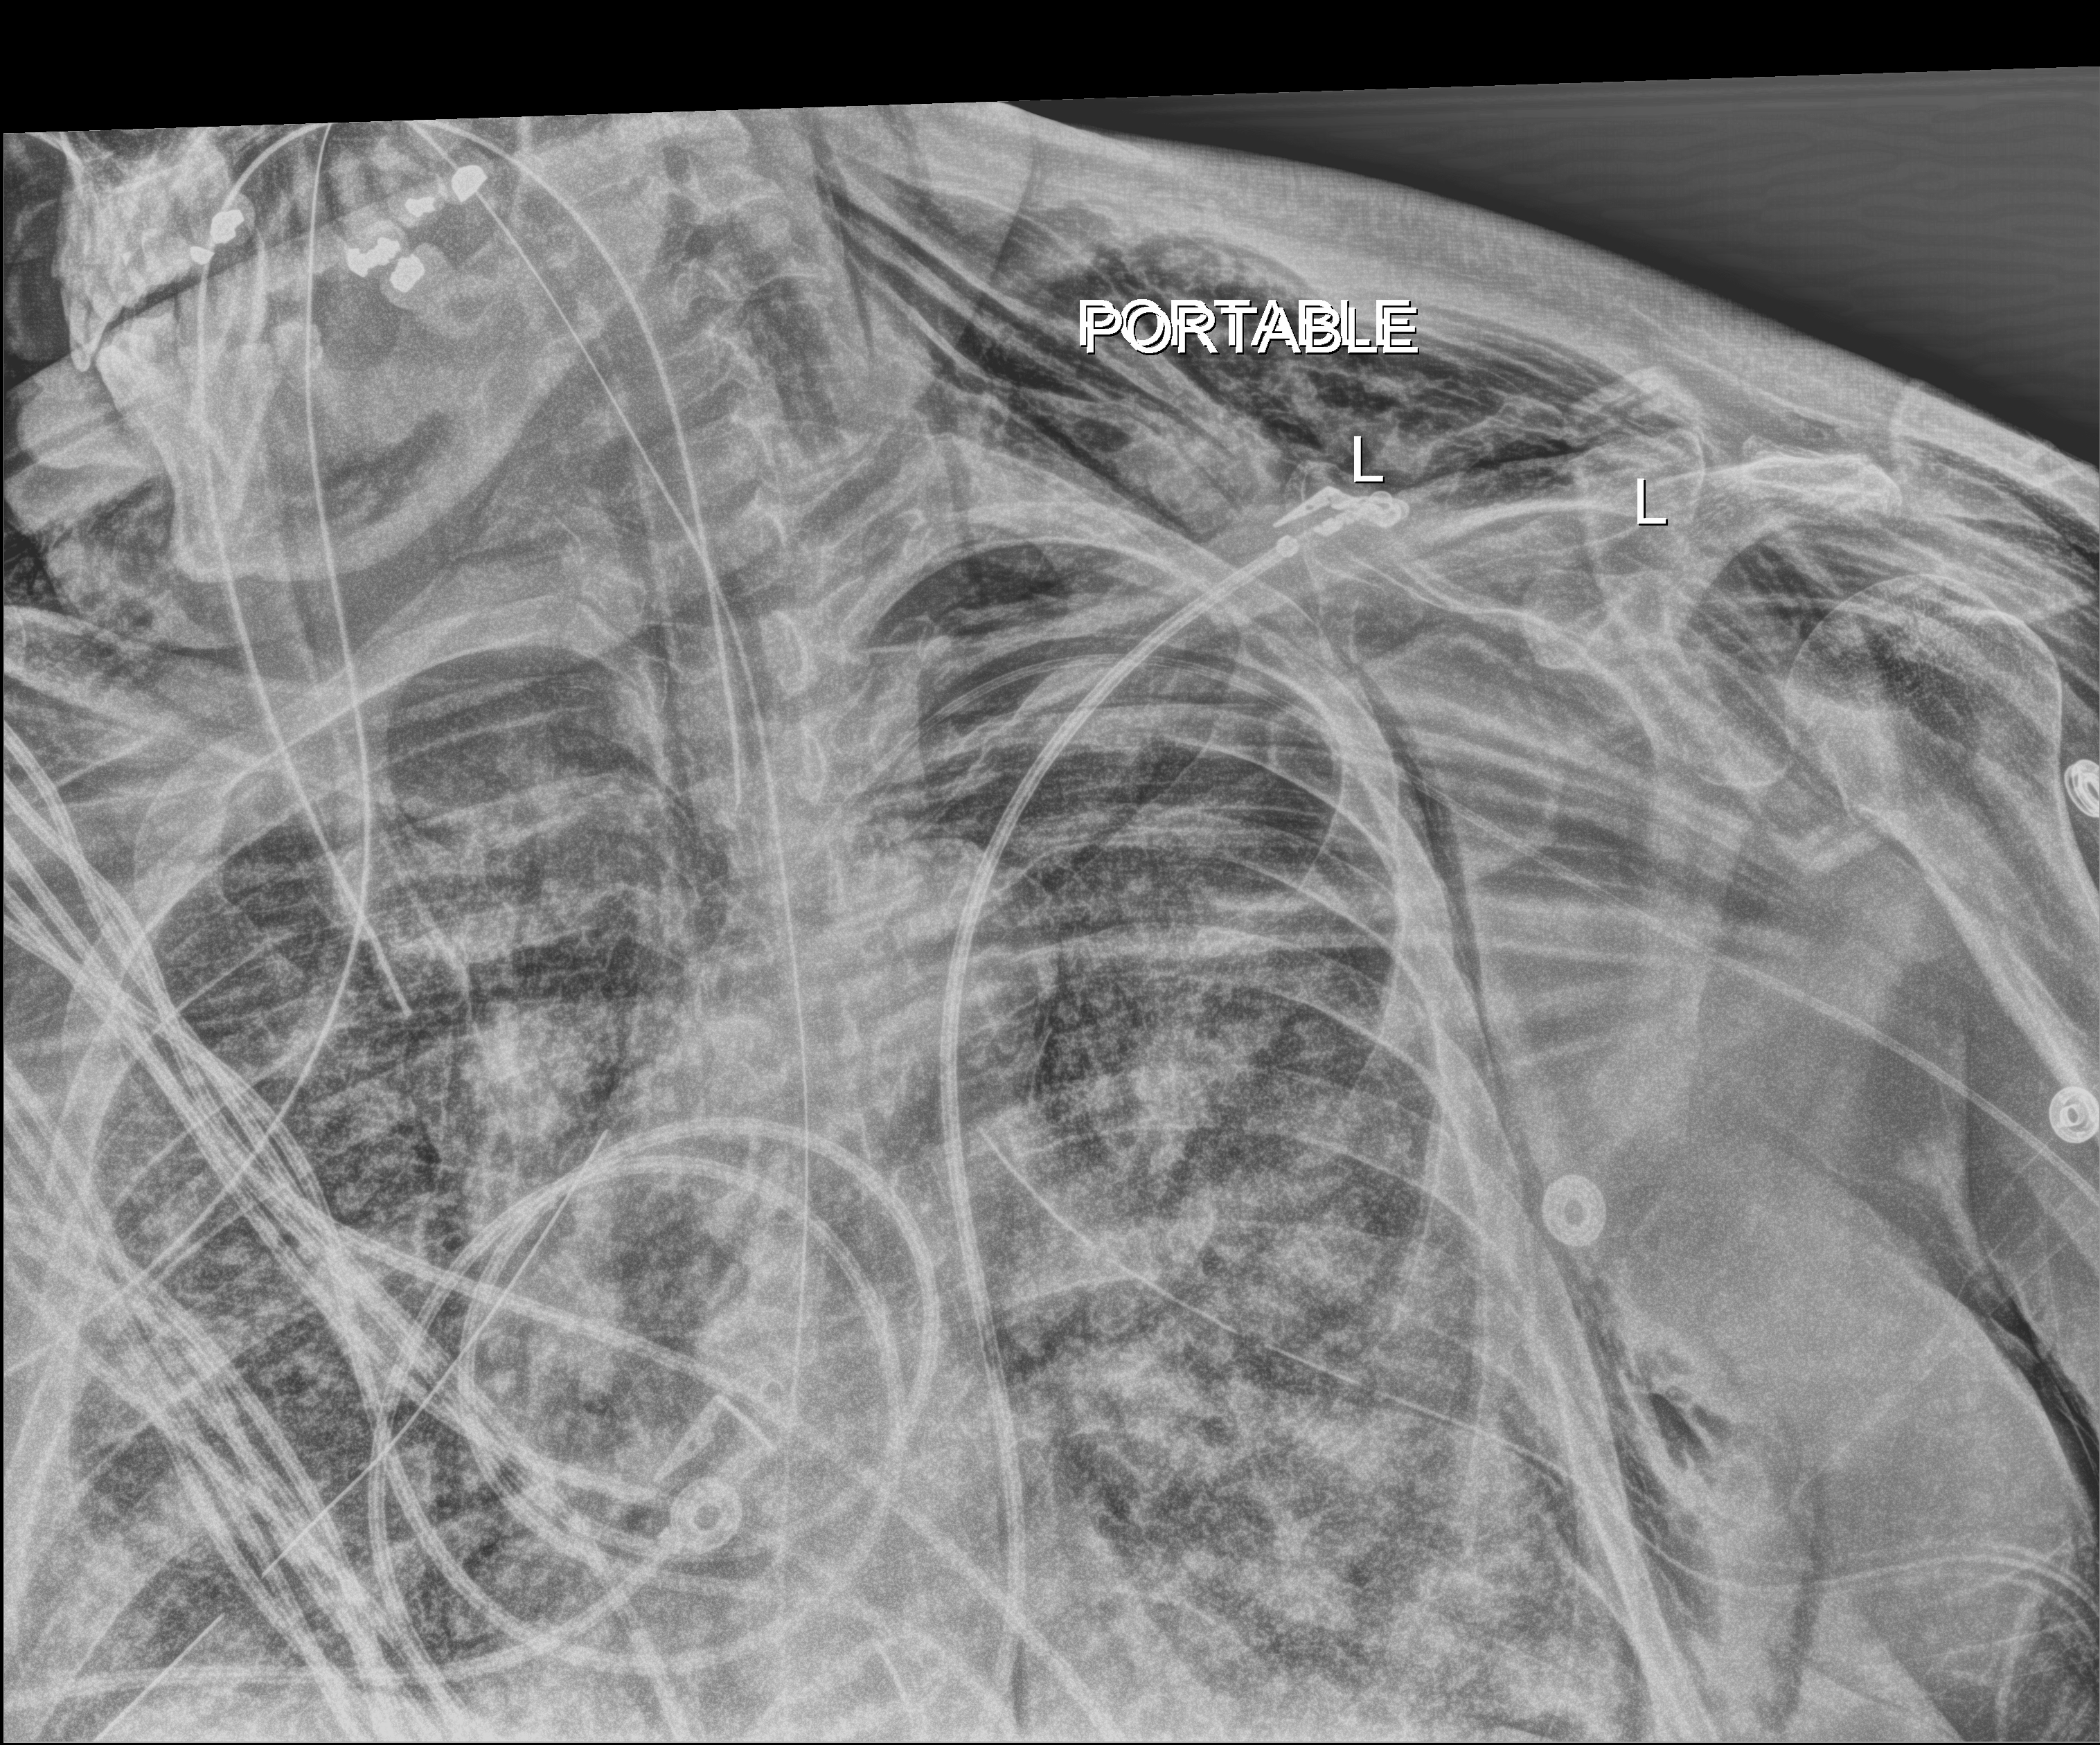
Chest radiograph (digital radiography), anteroposterior (AP) projection. Adult patient hospitalised with COVID-19, age 18–59 years.
Admission-level facts for this patient (not findings on this image; timing relative to this image not recorded): admitted to intensive care during this hospital stay: yes; mechanically ventilated during this hospital stay: yes.